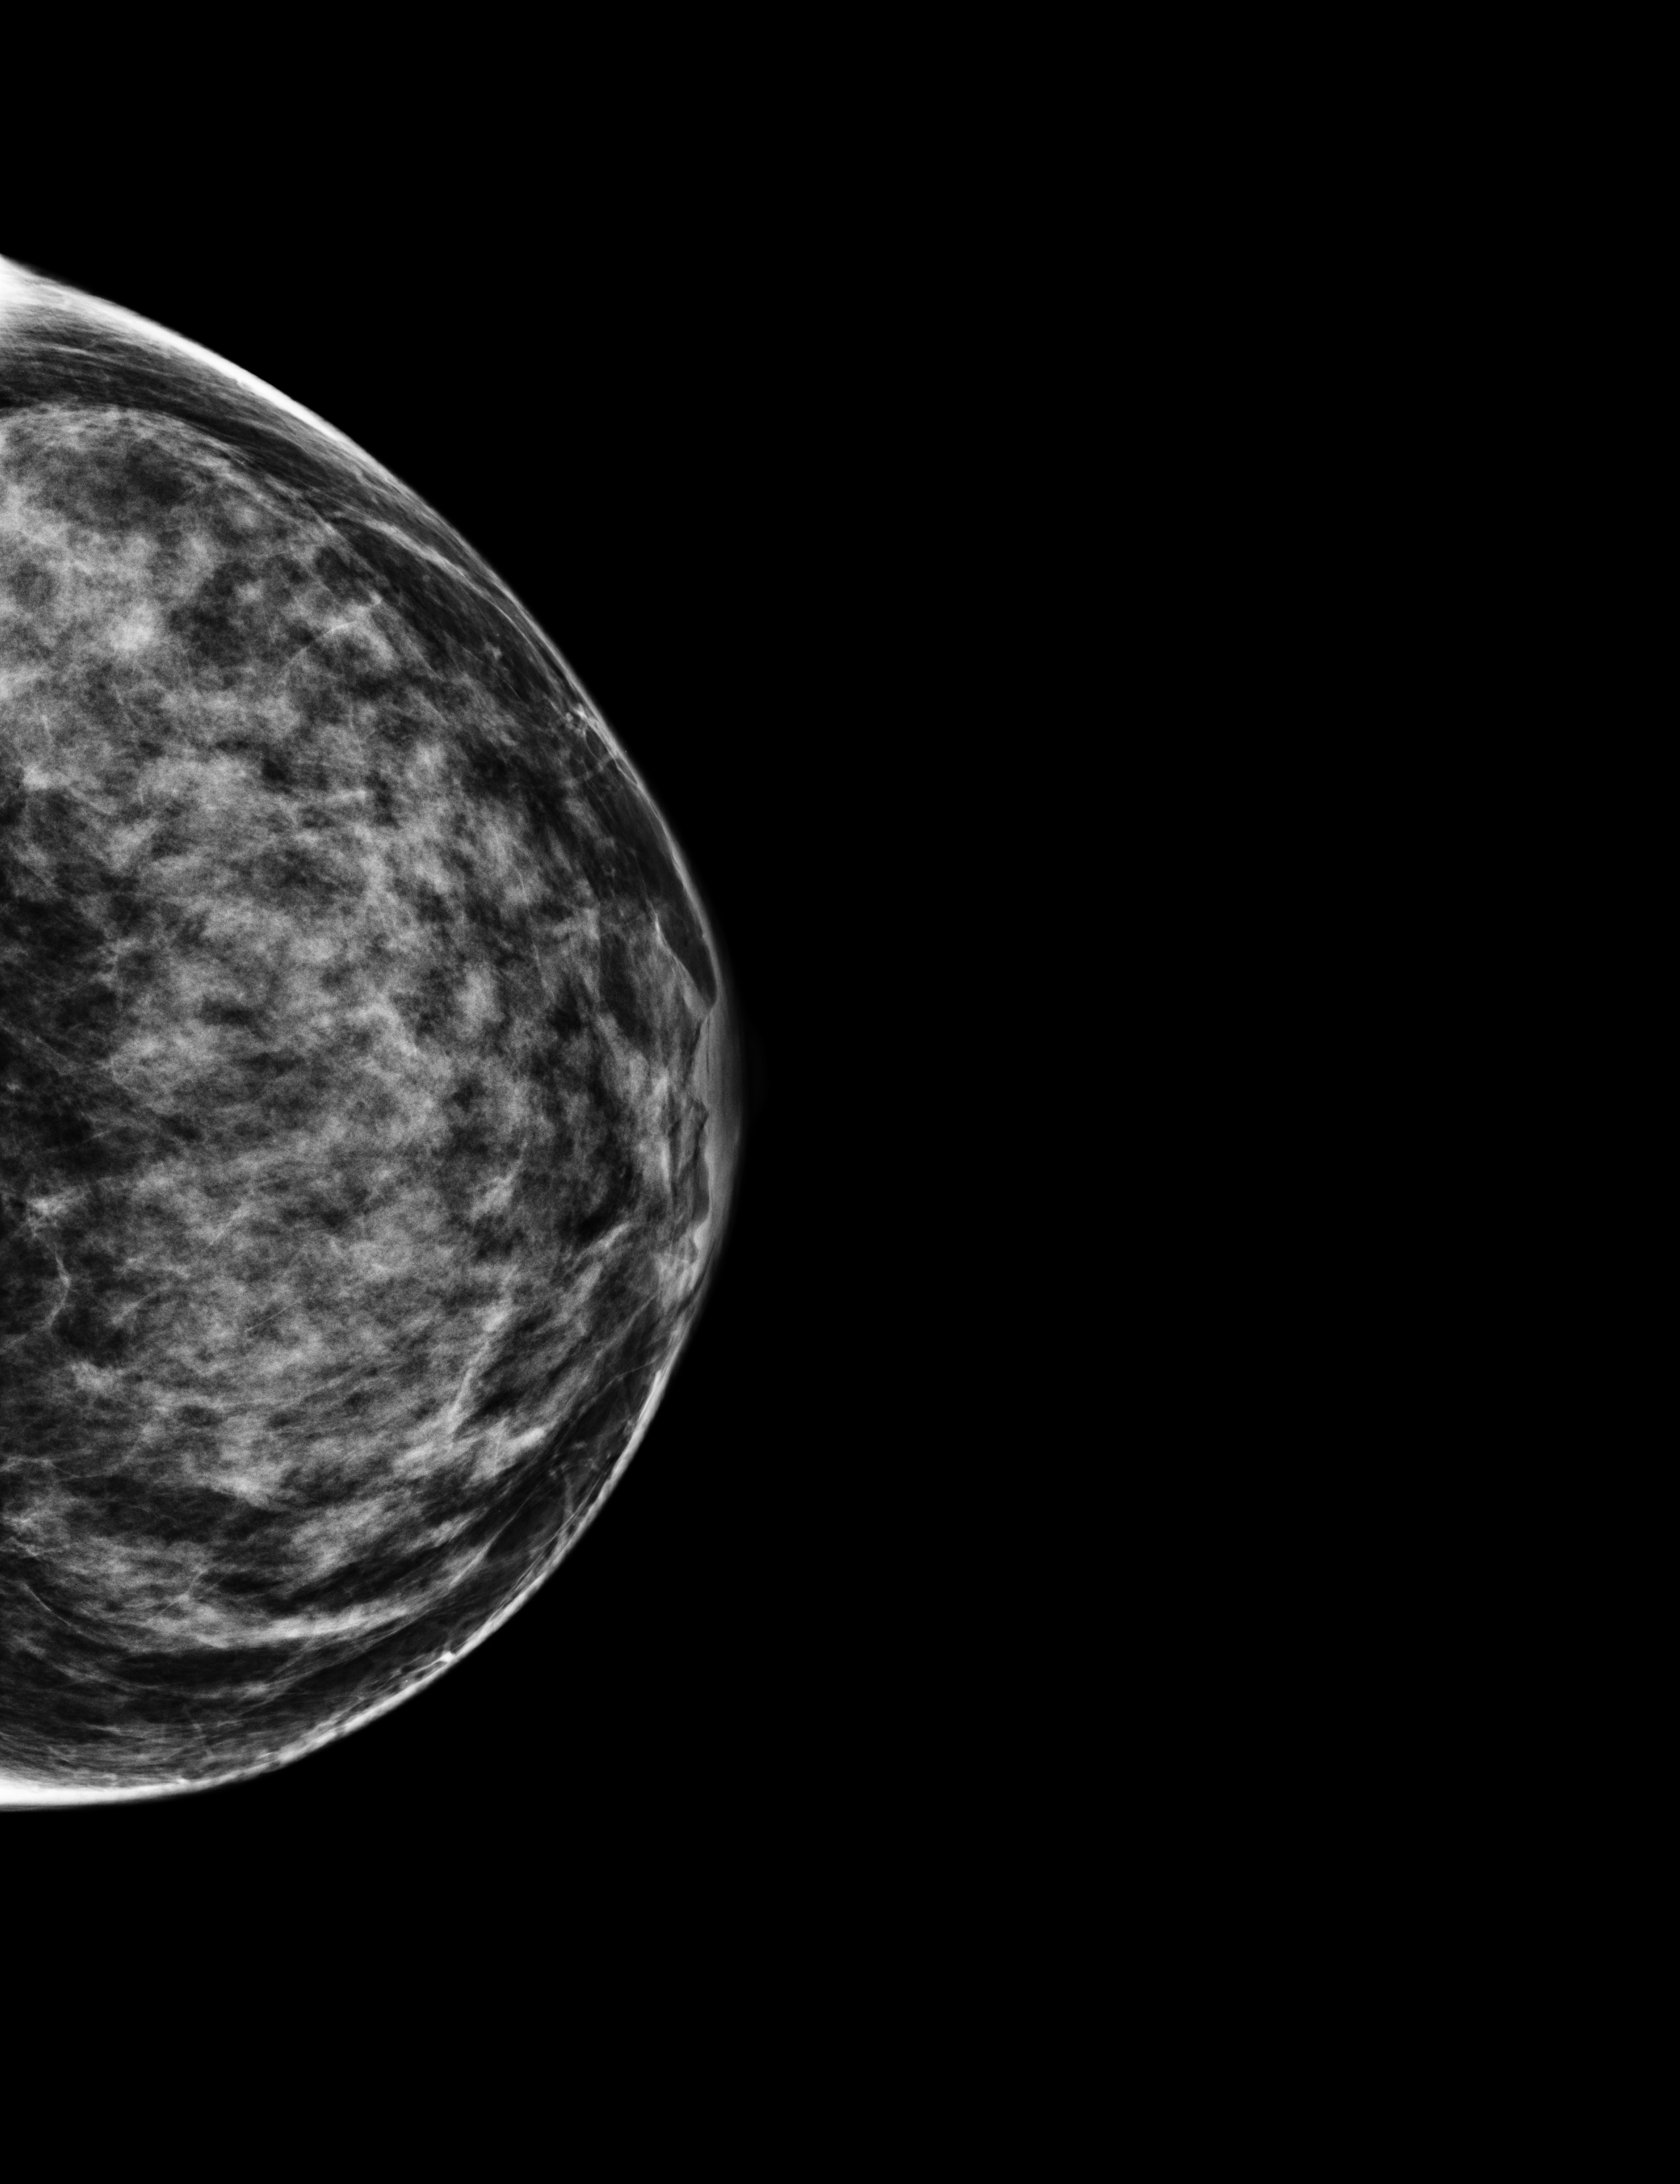
Digital mammogram (FFDM), left breast, craniocaudal (CC) view, screening examination, compressed breast thickness 56 mm. Patient aged 52 years (female).
BI-RADS breast density category at the screening exam (both breasts, scale 1–4): 3. Final BI-RADS category for the screening round (tomosynthesis exam, both breasts): category 2. Recall: recalled for additional imaging after this screen.